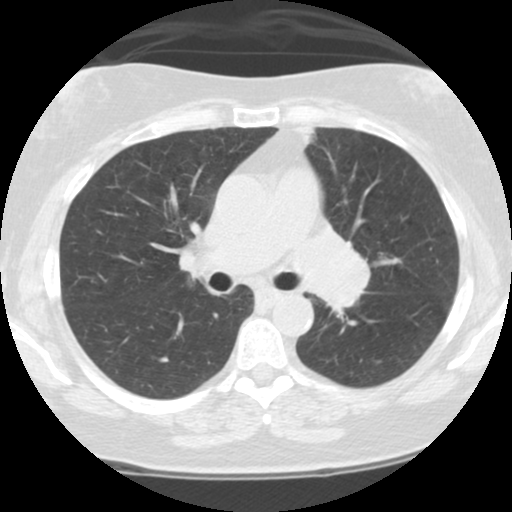
Low-dose screening chest CT, one axial slice; 120 kVp; lung window (W 1500 / L -600 HU); 2.5 mm slice thickness; 512 × 512 image matrix.
Structures marked on this image (expert manual segmentation):
- lesion 1 (tumor, hilum of left lung): bounding box (x1, y1, x2, y2) in pixels: (296, 230, 370, 316)